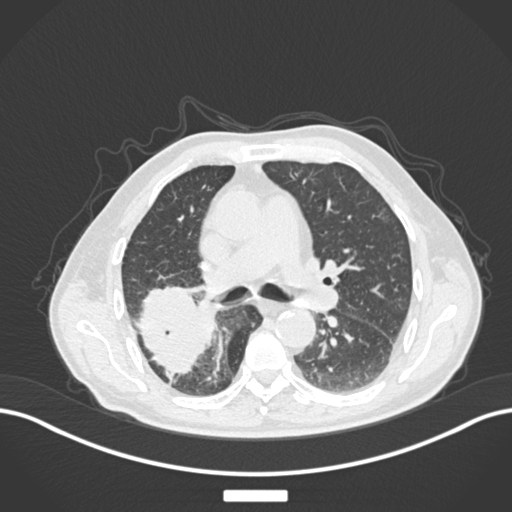
Chest CT, one axial slice; slice 103 of 201 in the series (ordered by position); reconstruction kernel B30f; lung window (W 1500 / L -600 HU); 1 mm slice thickness; 512 × 512 image matrix. Patient: male, 72 years. Case-level facts recorded for this patient, not image findings: clinical TNM (as recorded): T3 N2 M0.
Annotated regions visible in this slice (bounding box drawn by a radiologist):
- lung tumour (recorded histology: adenocarcinoma): bounding box [x1, y1, x2, y2] px = [132, 282, 212, 380]